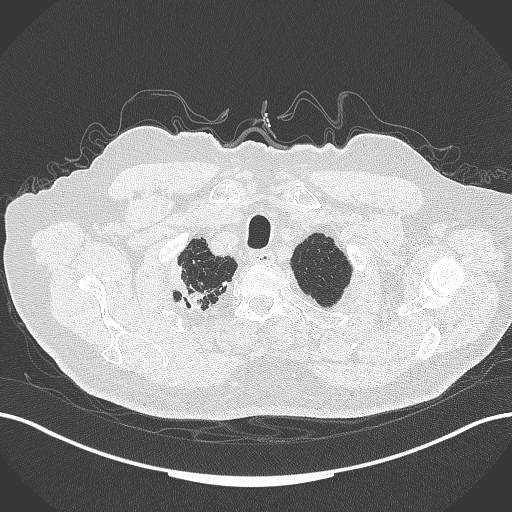
Chest CT, one axial slice; position 332 of 389 along the scan axis; 120 kVp; lung window (W 1500 / L -600 HU); 512 × 512 image matrix. Male patient, age 72 years. From the clinical record (not read from this slice): clinical TNM (as recorded): T1a N0 M0.
Outlined on this slice (bounding box drawn by a radiologist):
- lung tumour (recorded histology: squamous cell carcinoma): box from (x=163, y=257) to (x=209, y=310) px